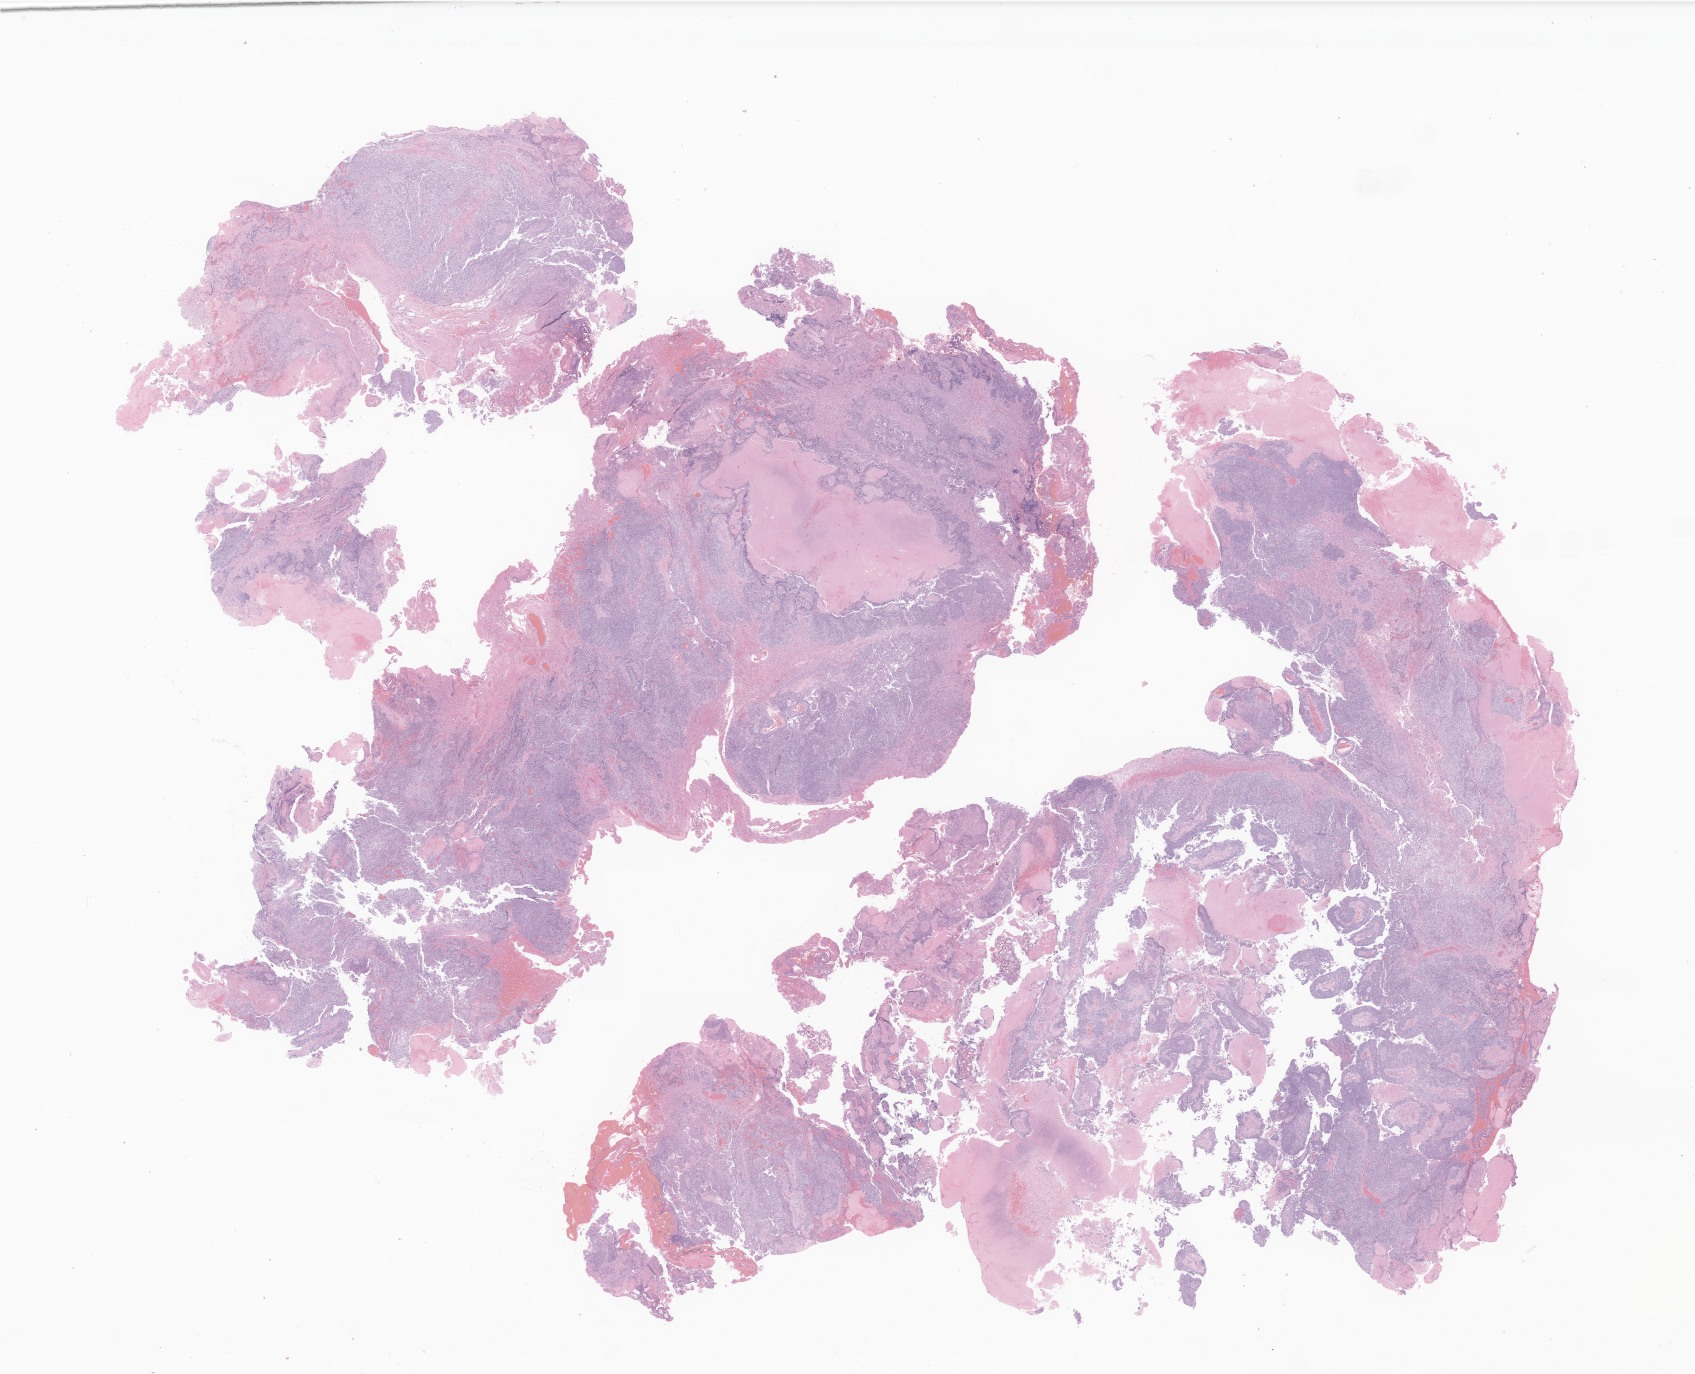
Digitized H&E-stained section of tumor tissue from the cerebral ventricle, shown as a low-resolution overview of the whole scanned area (about 28.6 x 23.2 mm), formalin-fixed, paraffin-embedded (FFPE) tissue. Patient male; age 478 days (about 1.3 years).
Diagnosis (ICD-O-3 morphology term): Atypical teratoid/rhabdoid tumor.